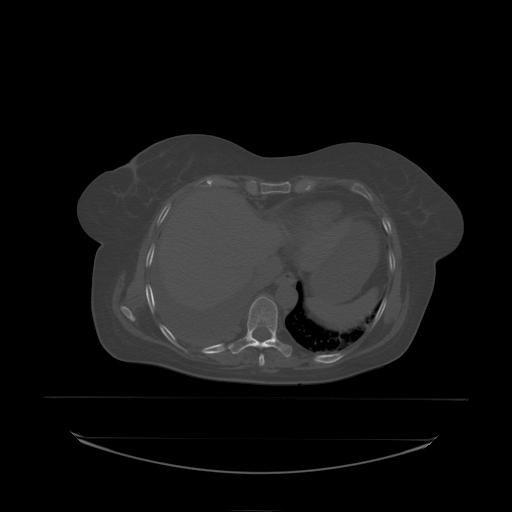
CT including the spine, one axial slice; slice 124 of 242 in the series (ordered by position); bone window (W 1800 / L 400 HU); 2.5 mm slice thickness; 512 × 512 image matrix. Patient: female, 53 years. From the clinical record (not read from this slice): primary cancer: lung; vertebrae with lytic lesions (as recorded): T7, L1.
Structures marked on this image (semi-automatic segmentation, software-assisted and operator-edited):
- T9 vertebra: box from (x=246, y=296) to (x=278, y=338) px